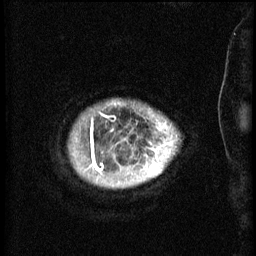
Breast MRI (dynamic contrast-enhanced), one sagittal slice; 3 images stored at this slice position (order not interpretable as contrast timing); 1.5 T; TE 4.2 ms, TR 8.2 ms; 256 × 256 image matrix, field of view 200 × 200 mm. Patient: female, 50 years.
Annotated regions visible in this slice (semi-automatically segmented with operator editing):
- analysis volume of interest (the breast-tissue region the enhancement analysis was run in; not a lesion): box from (x=74, y=108) to (x=169, y=187) px
- tumour enhancement mask (voxels above the 70 % enhancement threshold inside the analysis volume of interest): (x=96, y=148)–(x=161, y=175)